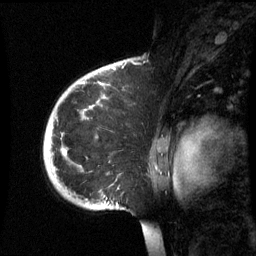
Breast MRI (dynamic contrast-enhanced), one sagittal slice; position 45 of 60 along the scan axis; dynamic contrast-enhanced series, image 2 of 3 at this slice position (ordered by acquisition); 1.5 T; TE 4.2 ms, TR 8.9 ms; 256 × 256 image matrix, field of view 220 × 220 mm. Patient: female, 35 years. Case-level facts recorded for this patient, not image findings: setting: breast cancer imaged before/during neoadjuvant chemotherapy; receptor status: HR-positive, HER2-negative.
Outlined on this slice (semi-automatic segmentation, software-assisted and operator-edited):
- analysis volume of interest (the breast-tissue region the enhancement analysis was run in; not a lesion): bounding box [x1, y1, x2, y2] px = [43, 74, 162, 215]
- tumour enhancement mask (voxels above the 70 % enhancement threshold inside the analysis volume of interest): [63, 154, 65, 157]